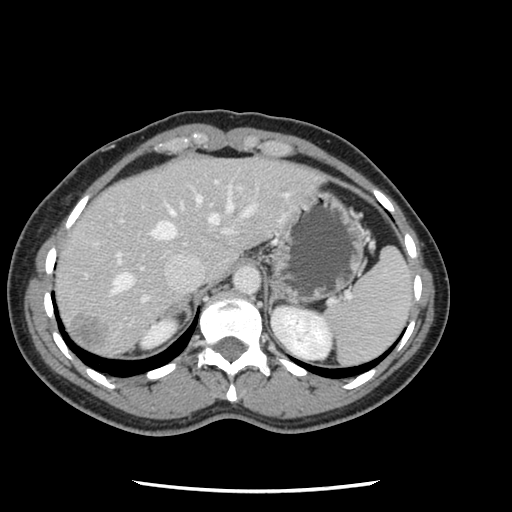
Contrast-enhanced abdominal CT, one axial slice; position 93 of 134 along the scan axis; 120 kVp; soft-tissue window (W 400 / L 40 HU); 2.5 mm slice thickness; 512 × 512 image matrix, field of view 330 × 330 mm. Female patient, age 43 years. From the clinical record (not read from this slice): diagnosis: colorectal cancer liver metastases, imaged before liver resection; multiple liver metastases: yes; largest metastasis: 3.4 cm; disease in both lobes: yes.
Structures marked on this image (manually delineated by an expert):
- hepatic veins: bounding box [x1, y1, x2, y2] px = [111, 194, 256, 294]
- liver: [56, 157, 318, 358]
- planned liver remnant (the part of the liver to remain after resection): [56, 163, 193, 309]
- portal vein (with intrahepatic branches): [84, 180, 236, 303]
- liver metastasis: [70, 317, 105, 352]